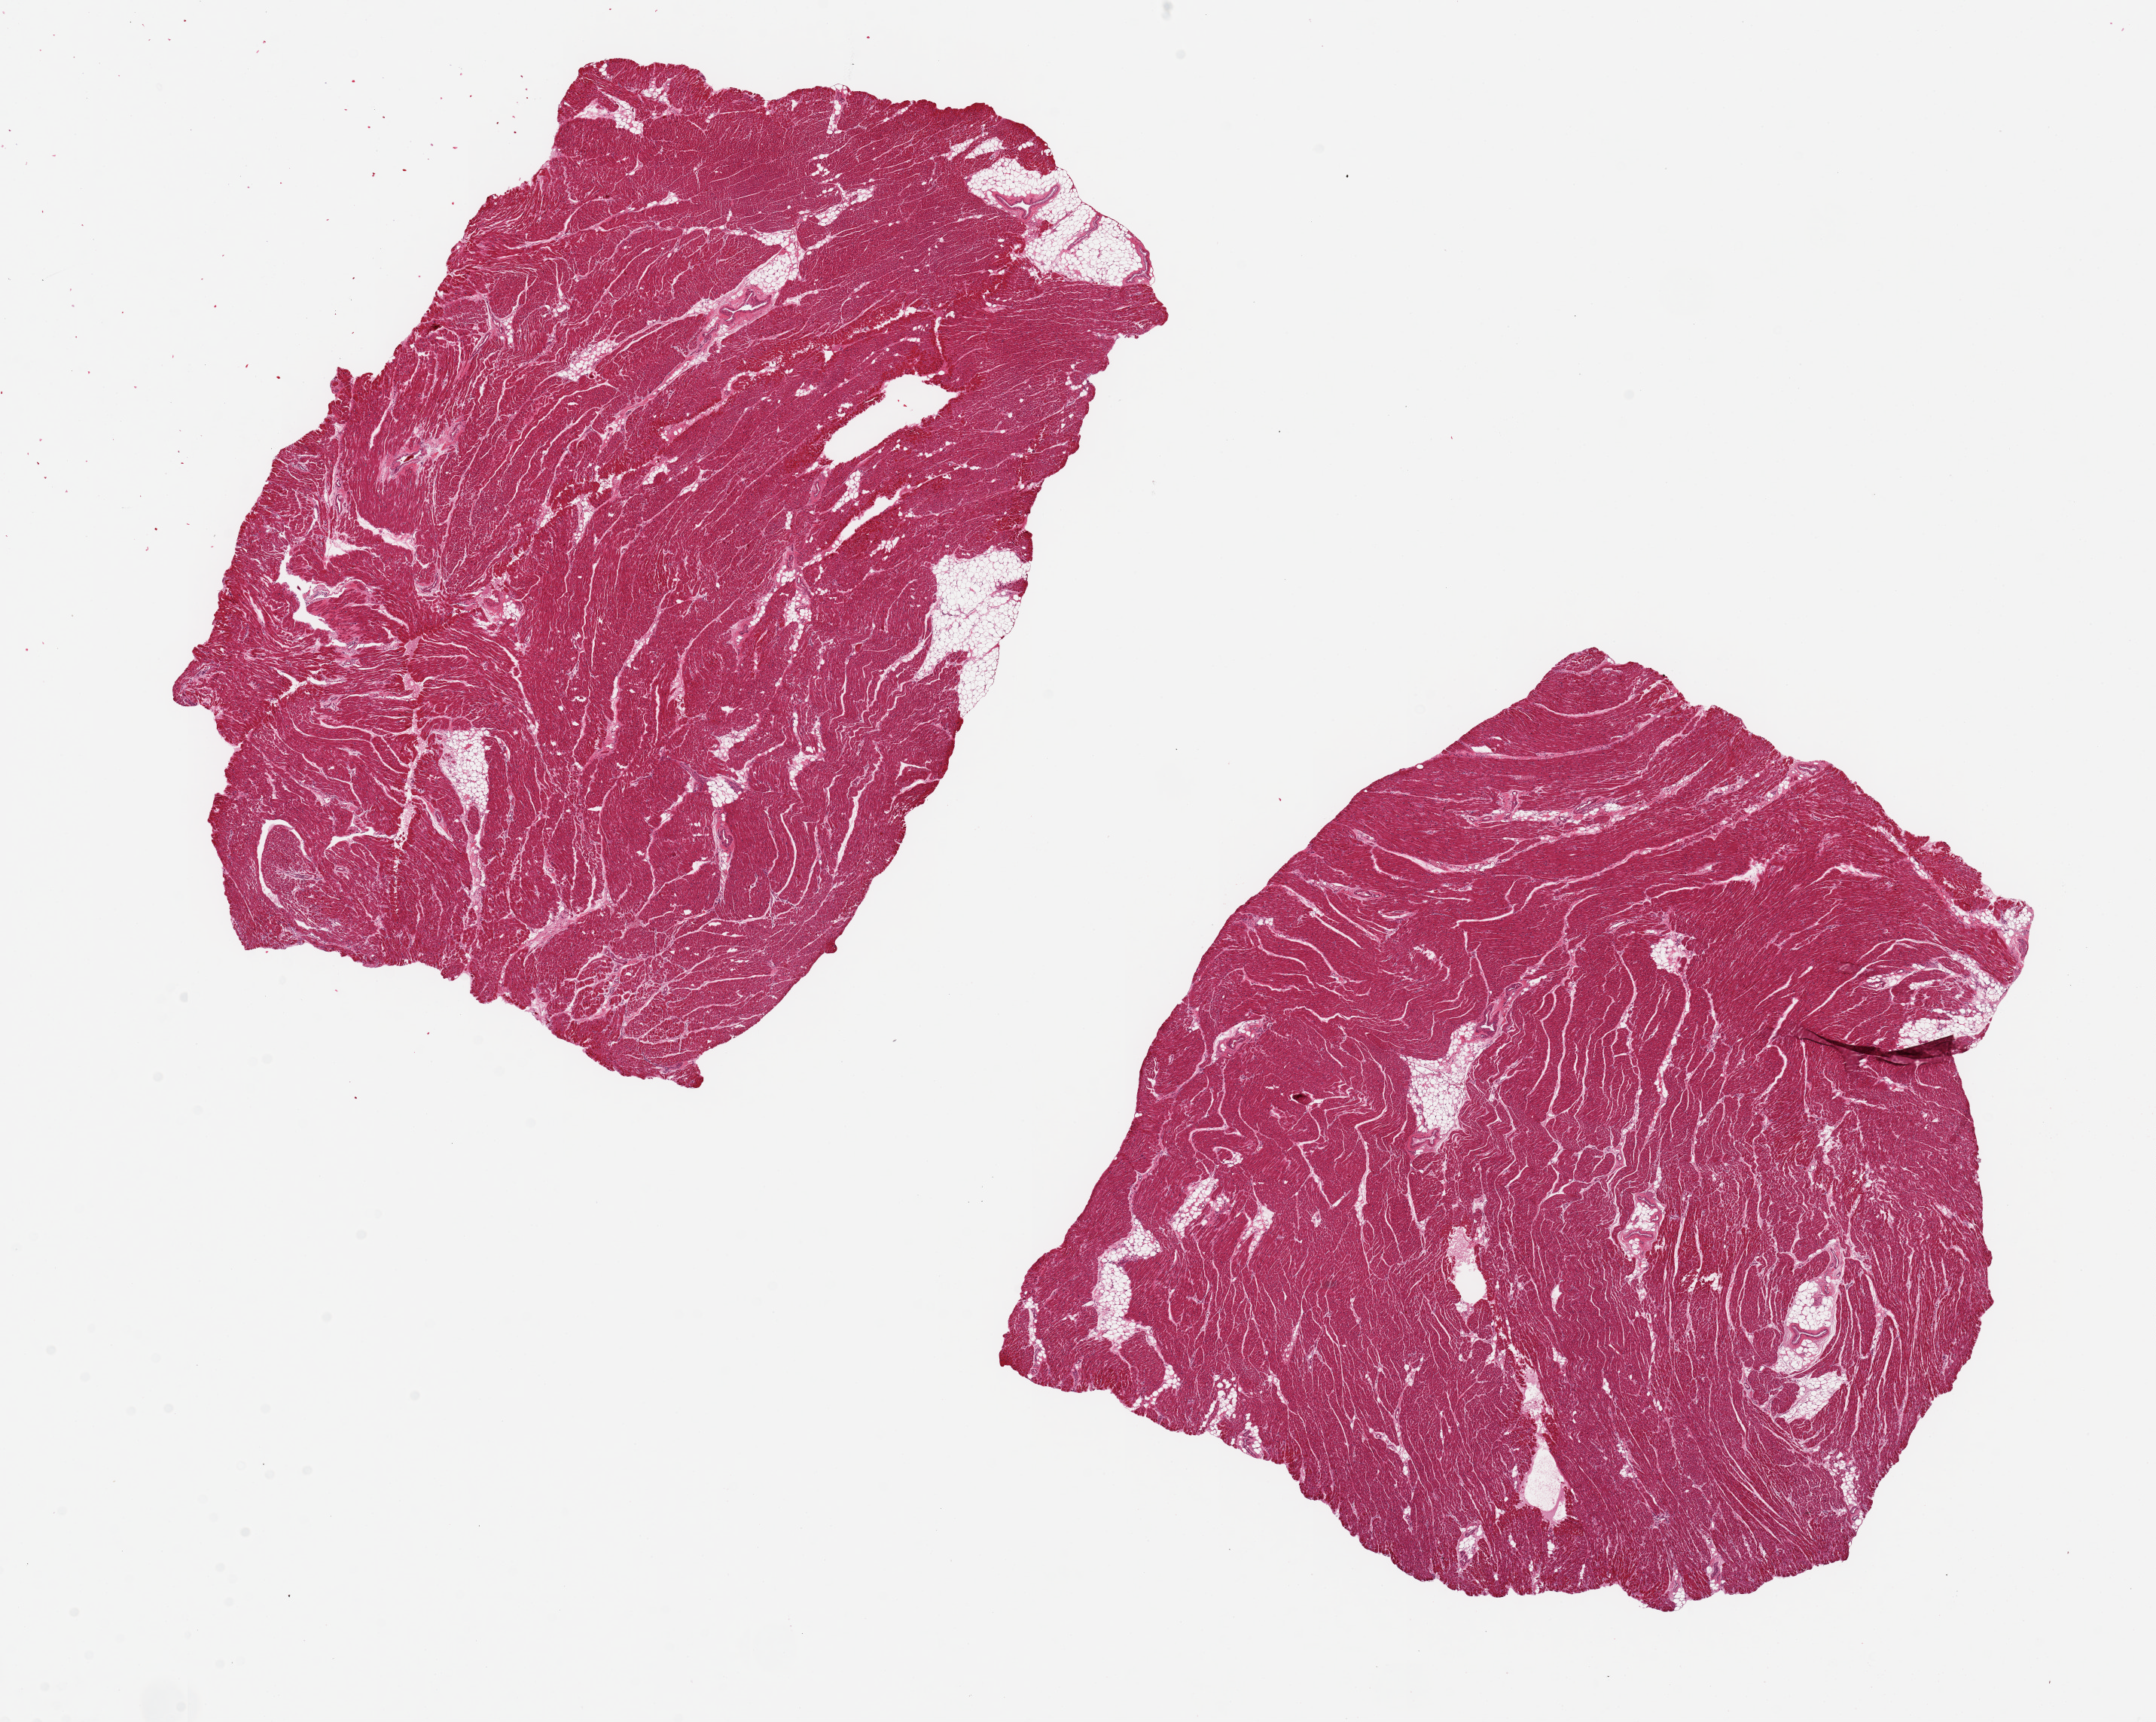
Digitized hematoxylin and eosin (H&E)-stained section — low-resolution overview of the scanned area, about 22.6 x 18.1 mm (acquisition: 20x scan); PAXgene-fixed paraffin-embedded (PFPE) section; section of heart (target tissue); tissue donor sample. Donor sex: female.
Review note (as recorded): 2 pieces, 10x9 & 11x8mm; minimal interstitial fibrosis.